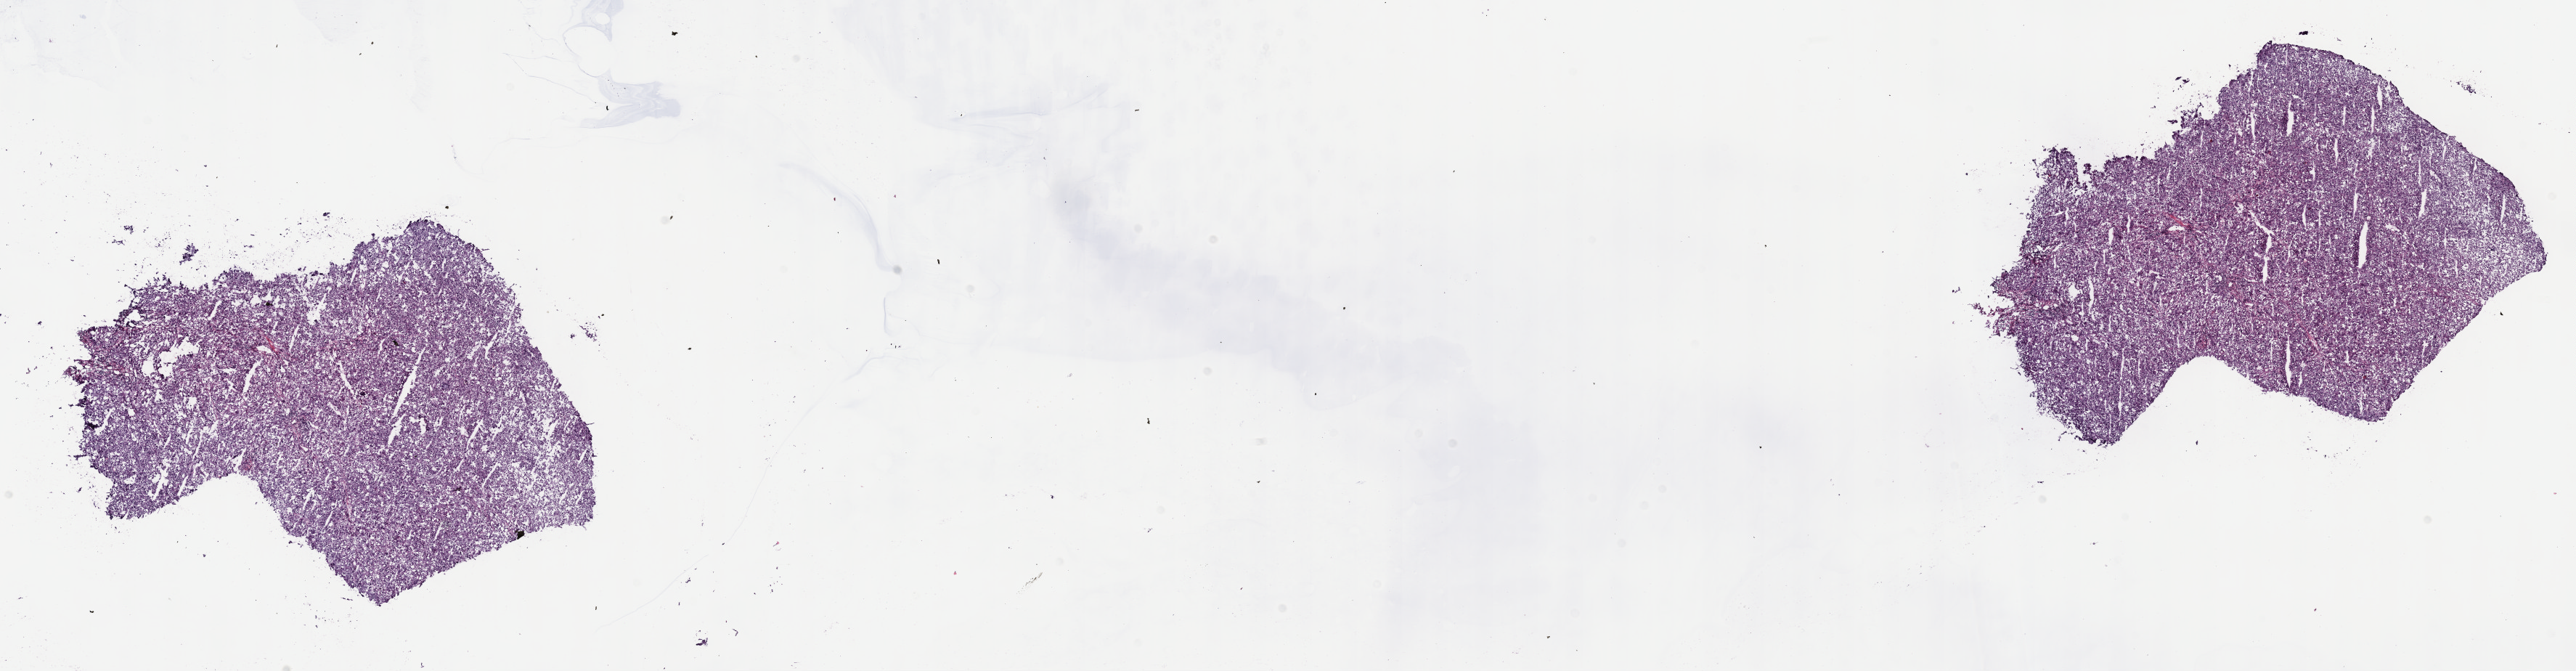
Whole-slide histology image, Hematoxylin and eosin (H&E) stained — shown as a low-resolution overview of the whole scanned area (about 28.7 x 7.5 mm). Frozen section from the top of the tissue portion. Liver, primary tumour sample. Female patient; age at initial diagnosis 69 years. Histologic grade: G2 (moderately differentiated). Pathologist review of this section (percent, as recorded): tumour cells 100%, tumour nuclei 95%, normal cells 0%, stromal cells 0%, necrosis 0%. Infiltration values recorded for this section: lymphocyte infiltration 0%, monocyte infiltration 0%, neutrophil infiltration 0%.
* pathologic diagnosis: Hepatocellular carcinoma, NOS
* AJCC pathologic stage: I